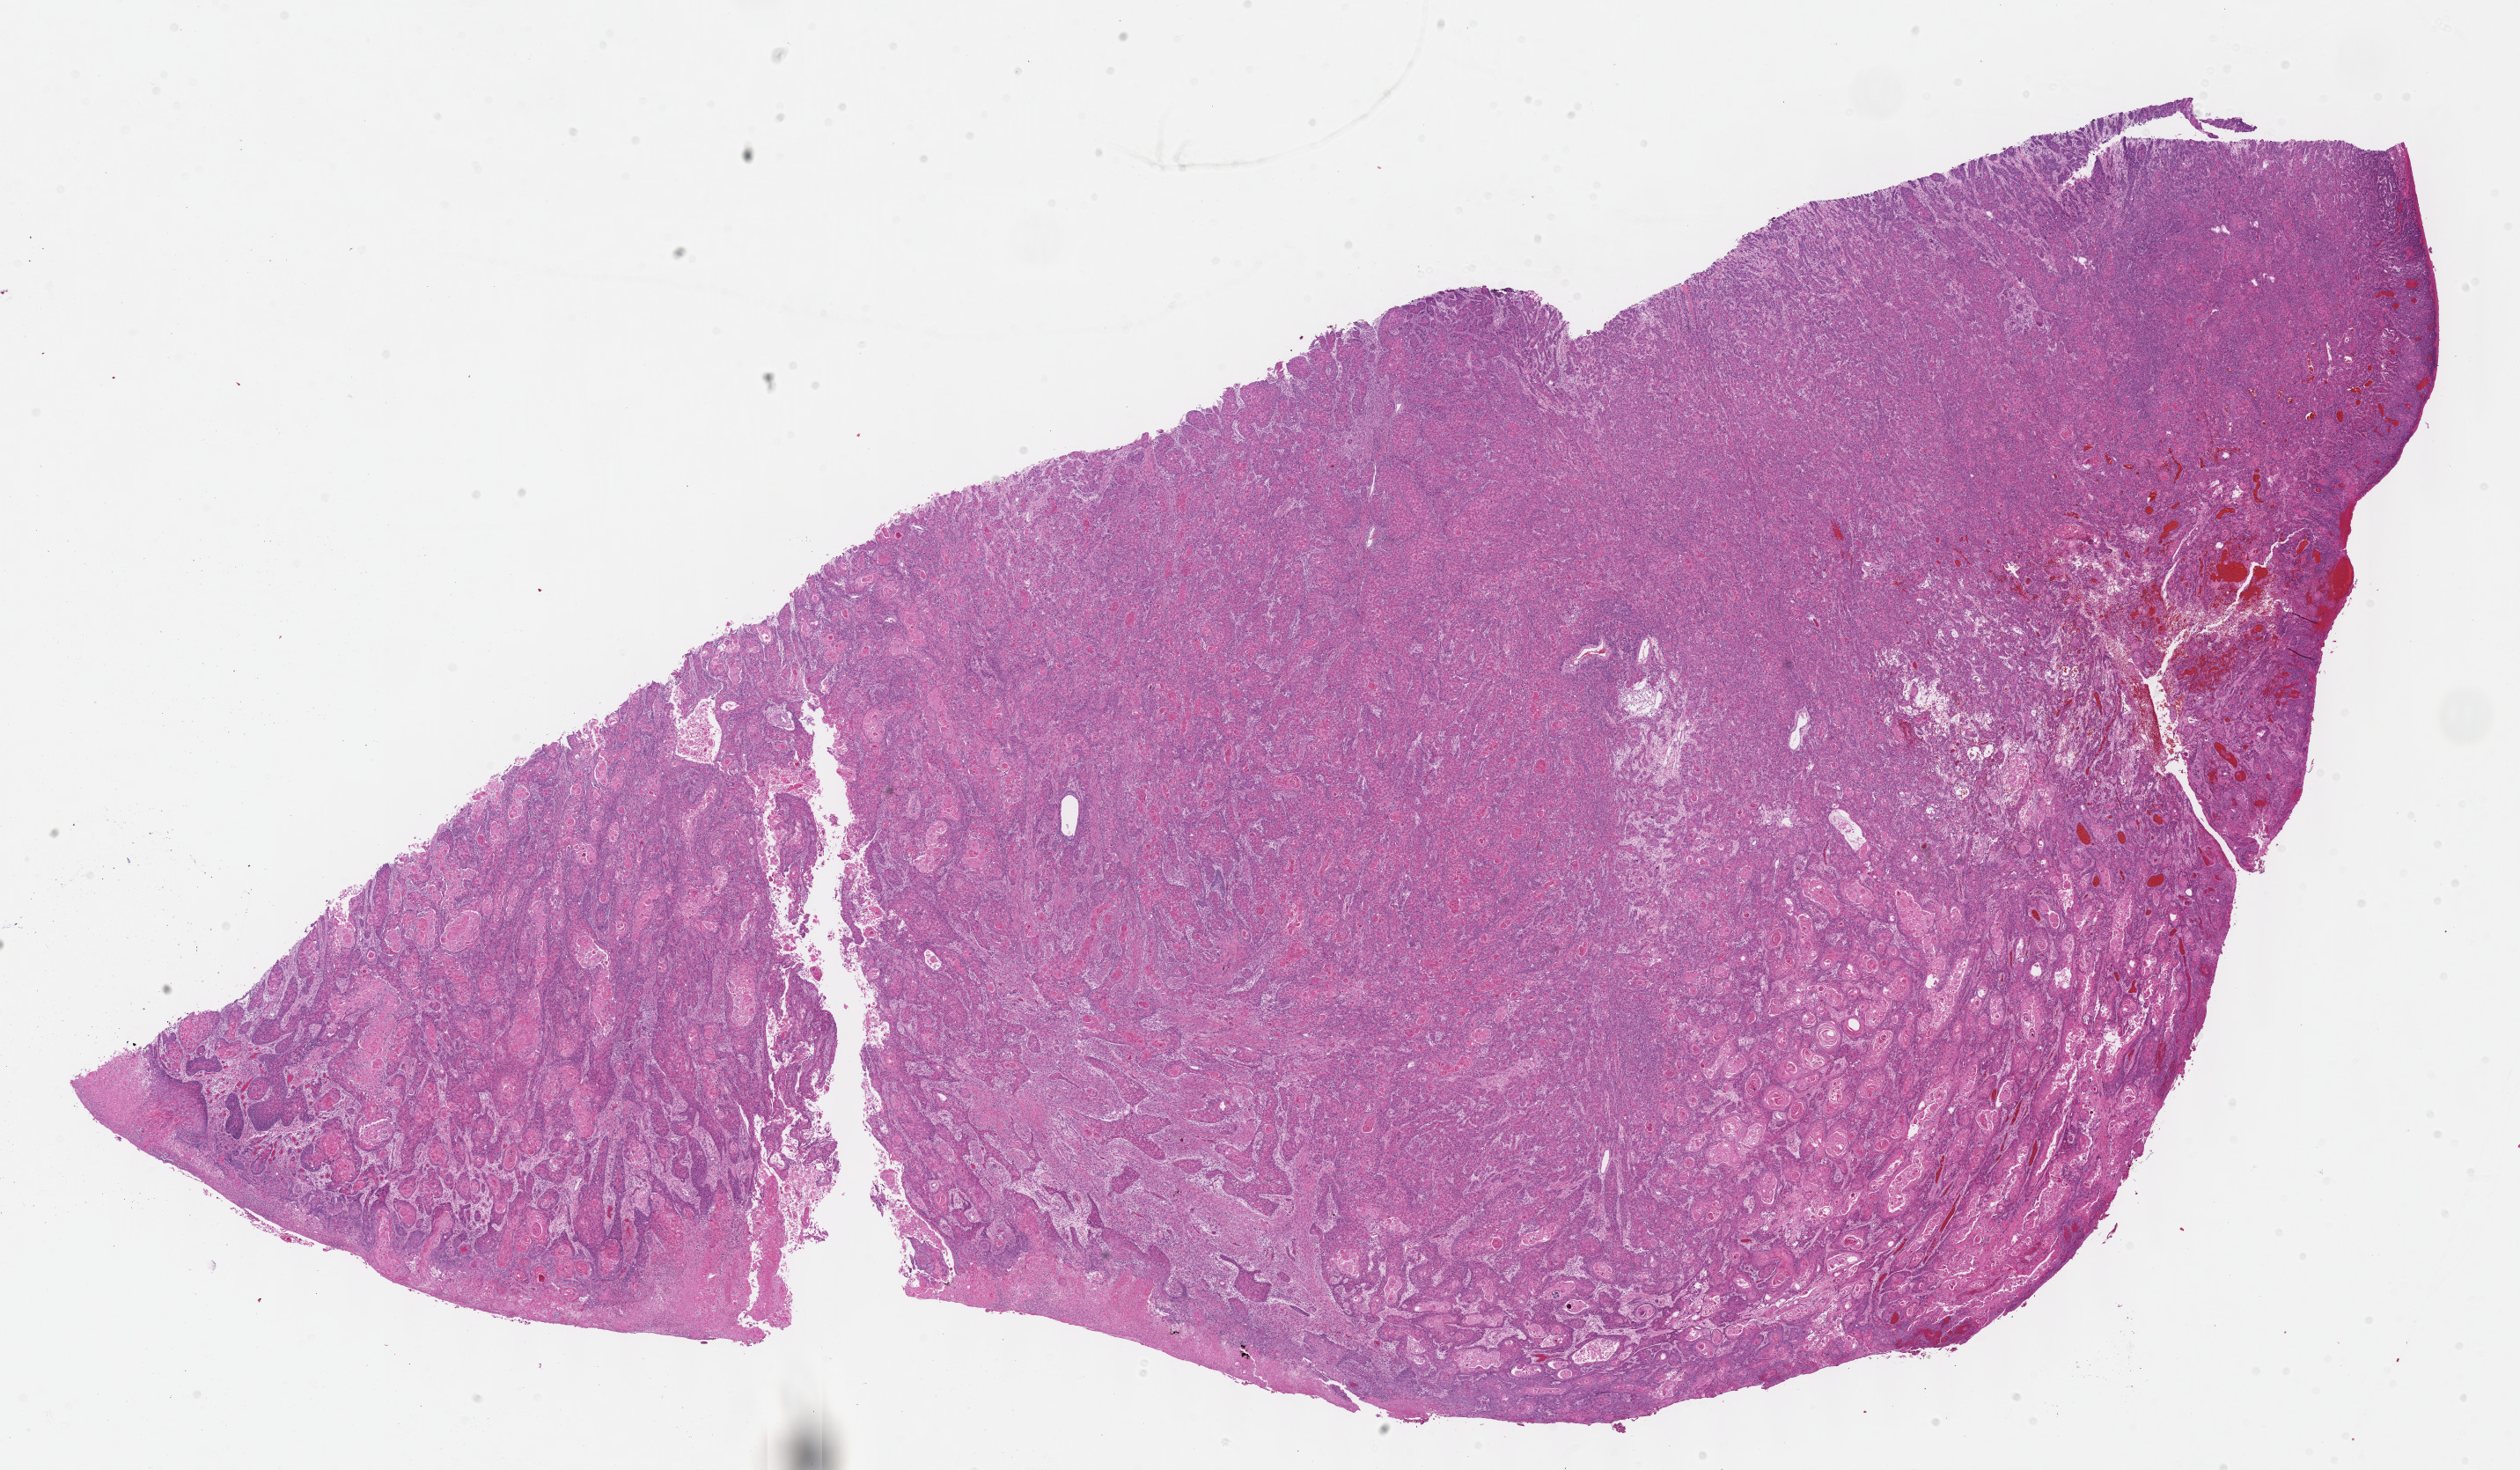
Digitized H&E-stained tissue section (whole slide) — whole scanned area (about 23.1 x 13.5 mm) shown as a low-resolution overview. FFPE section. Head and neck, primary tumour sample. Female, age 61 years at initial diagnosis. Histologic grade: G2 (moderately differentiated).
AJCC pathologic stage: IVA (7th edition). Pathologic diagnosis: Squamous cell carcinoma, NOS (tongue, NOS).